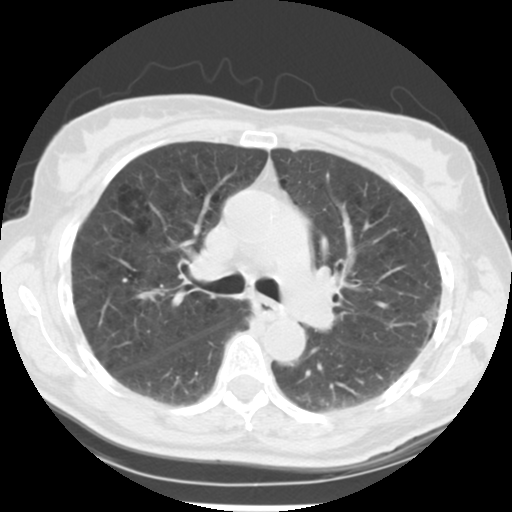
Low-dose screening chest CT, one axial slice. Slice 138 of 223 in the series (ordered by position). 120 kVp. Lung window (W 1500 / L -600 HU). 2.5 mm slice thickness. 512 × 512 image matrix.
Structures marked on this image (manually delineated by an expert):
- lesion 1 (tumor, upper lobe of left lung): box from (x=423, y=294) to (x=441, y=328) px